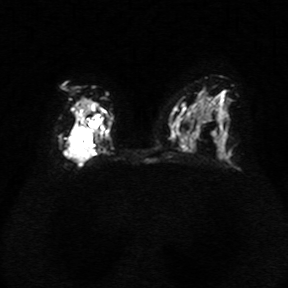
Breast MRI, one axial slice; slice 18 of 34 in the series (ordered by position); diffusion-weighted series; image 2 of 4 stored at this slice position (different b-values; order by instance number); 1.5 T; 5 mm slice thickness; 288 × 288 image matrix. Female patient.
Annotated regions visible in this slice (manually delineated by an expert):
- tumour on diffusion-weighted imaging: box from (x=62, y=119) to (x=101, y=162) px